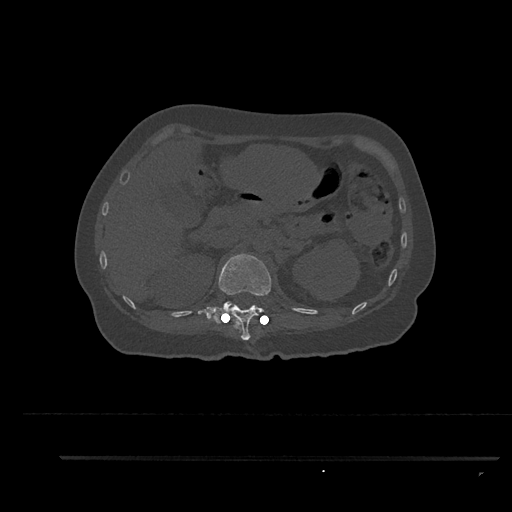
CT including the spine, one axial slice; slice 246 of 797 in the series (ordered by position); 120 kVp; bone window (W 1800 / L 400 HU); 0.5 mm slice thickness; 512 × 512 image matrix, field of view 408 × 408 mm. Patient: female, 44 years. Case-level facts recorded for this patient, not image findings: primary cancer: renal; vertebrae with lytic lesions (as recorded): L1.
Outlined on this slice (semi-automatic segmentation, software-assisted and operator-edited):
- L1 vertebra: bounding box (x1, y1, x2, y2) in pixels: (224, 301, 232, 309)
- T12 vertebra: (198, 253, 271, 340)